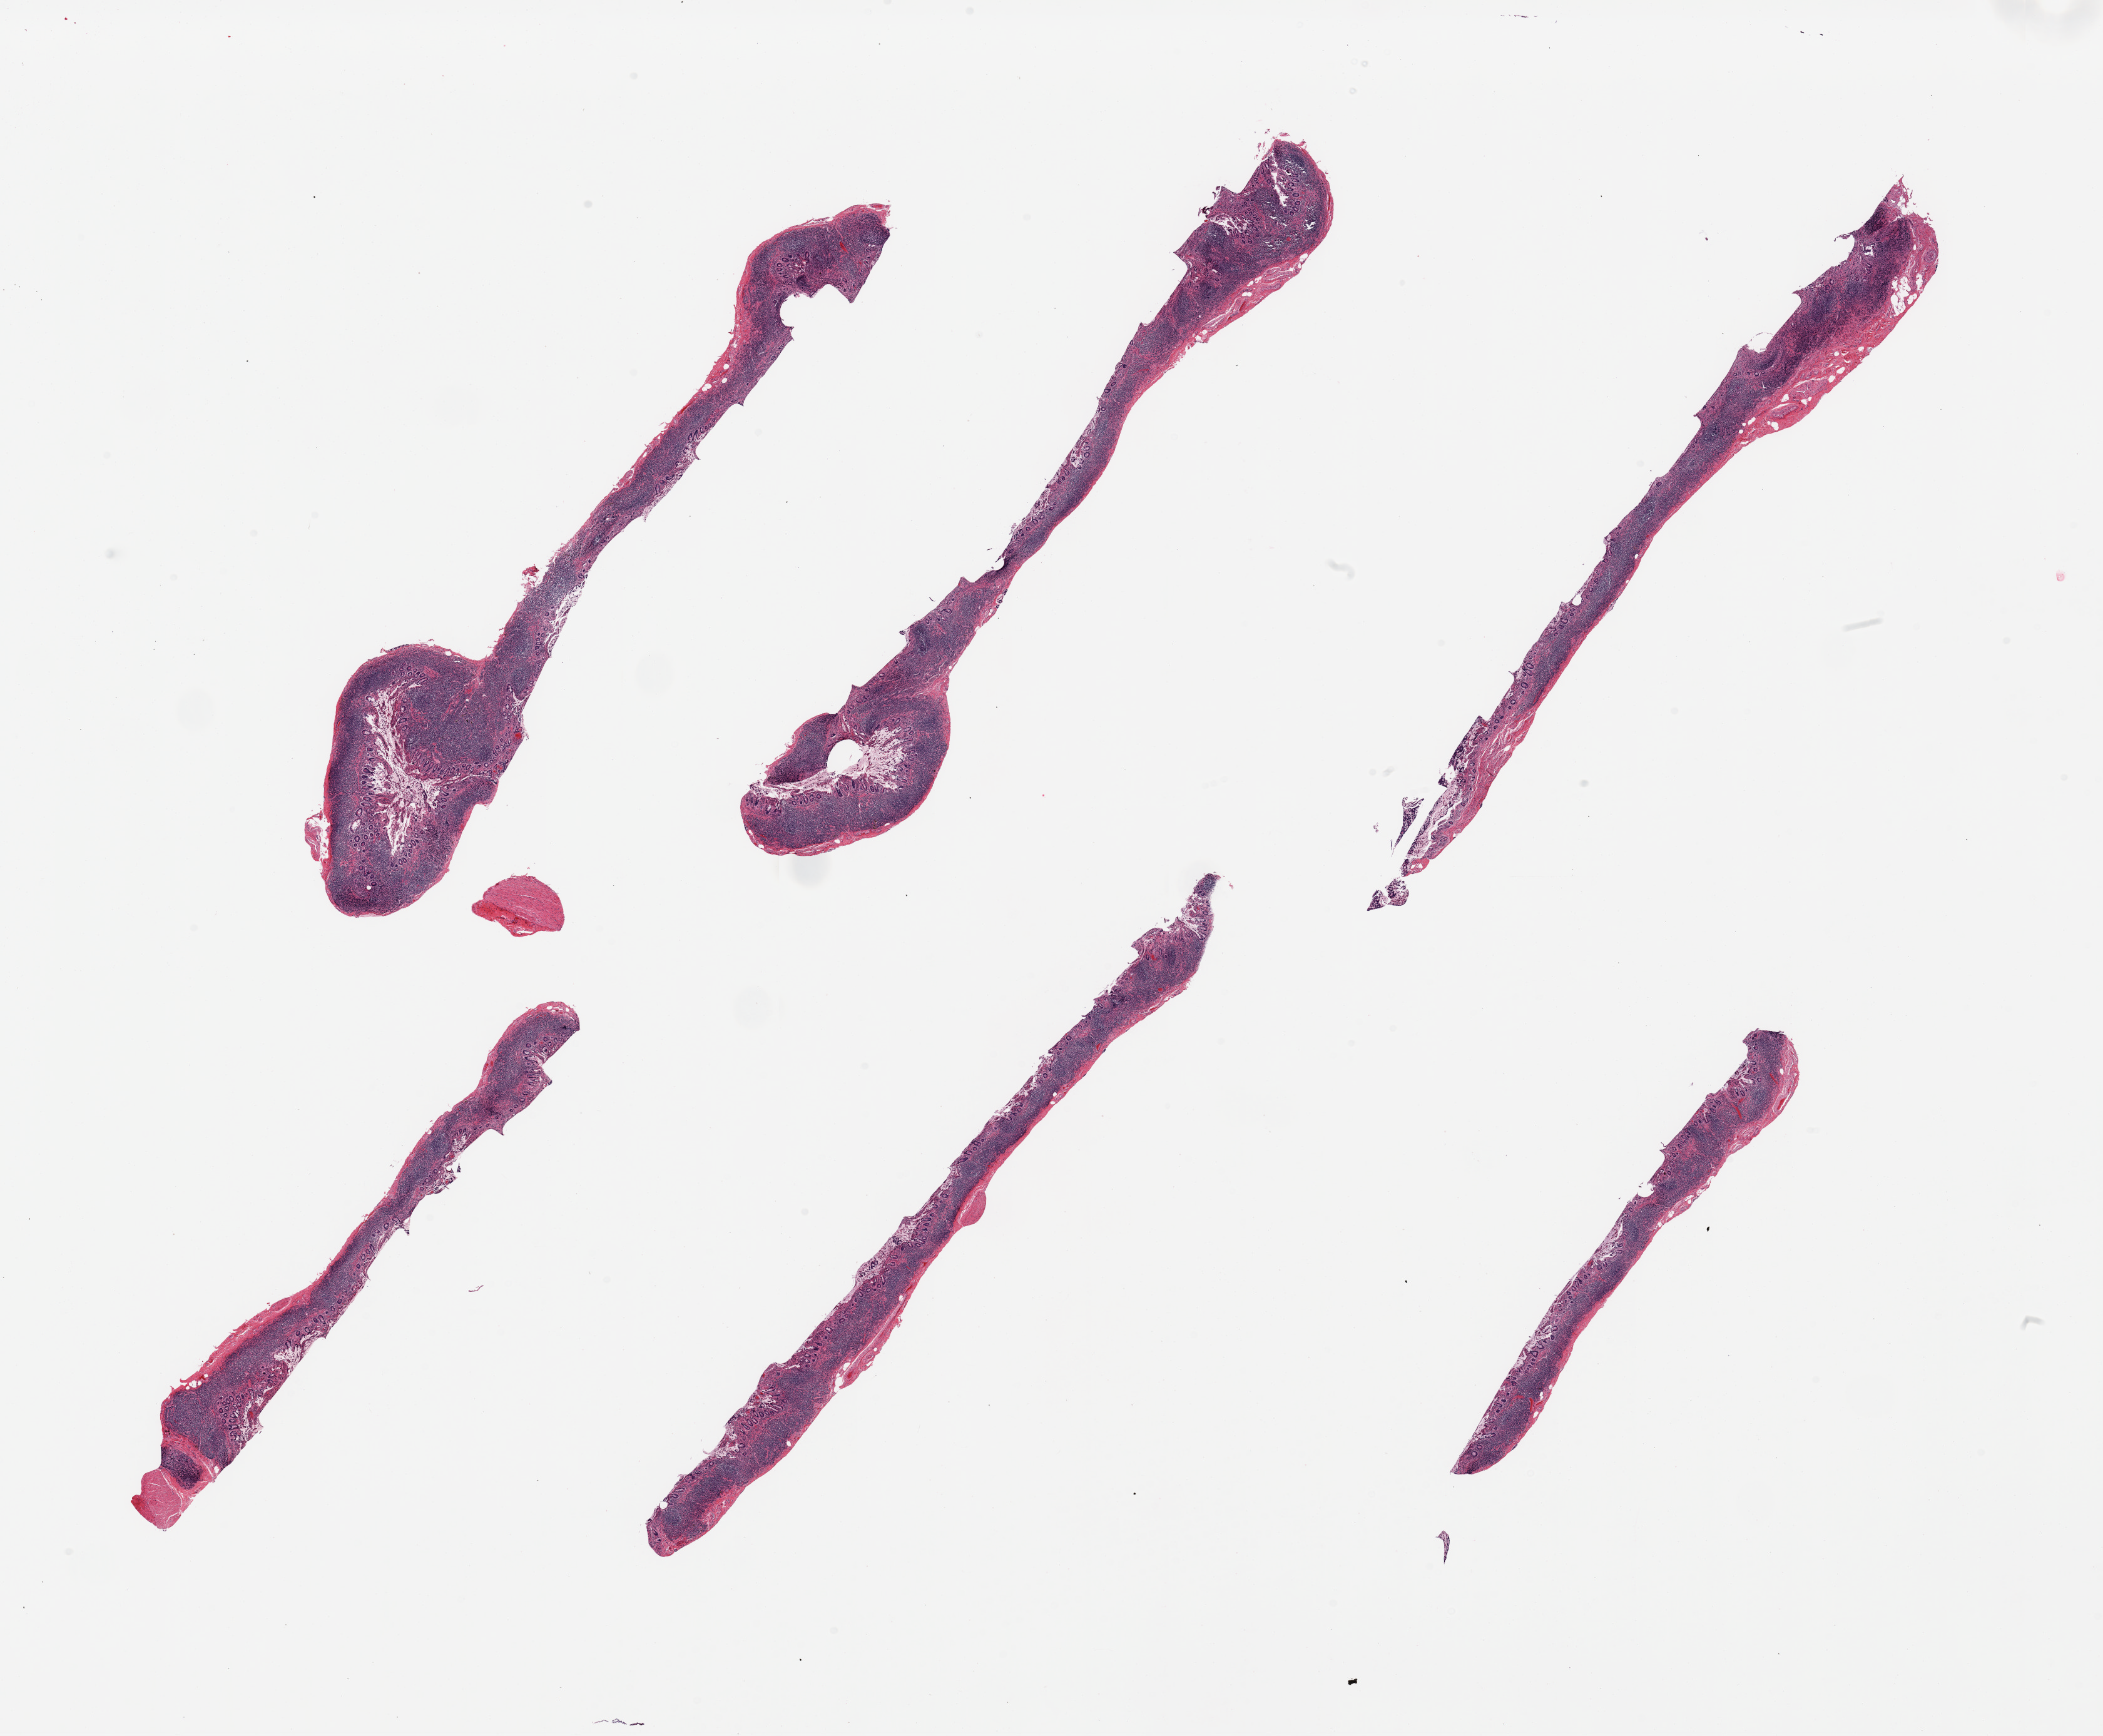
Digitized hematoxylin and eosin (H&E)-stained section, shown as a low-resolution overview of the whole scanned area (about 26.6 x 21.9 mm, acquisition: 20x scan), PAXgene-fixed paraffin-embedded (PFPE) section, target tissue: ileum, donor tissue sample. Male donor.
- review note (as recorded): 6 pieces, abundant lymphoid aggregates are ~60-70% of tissue